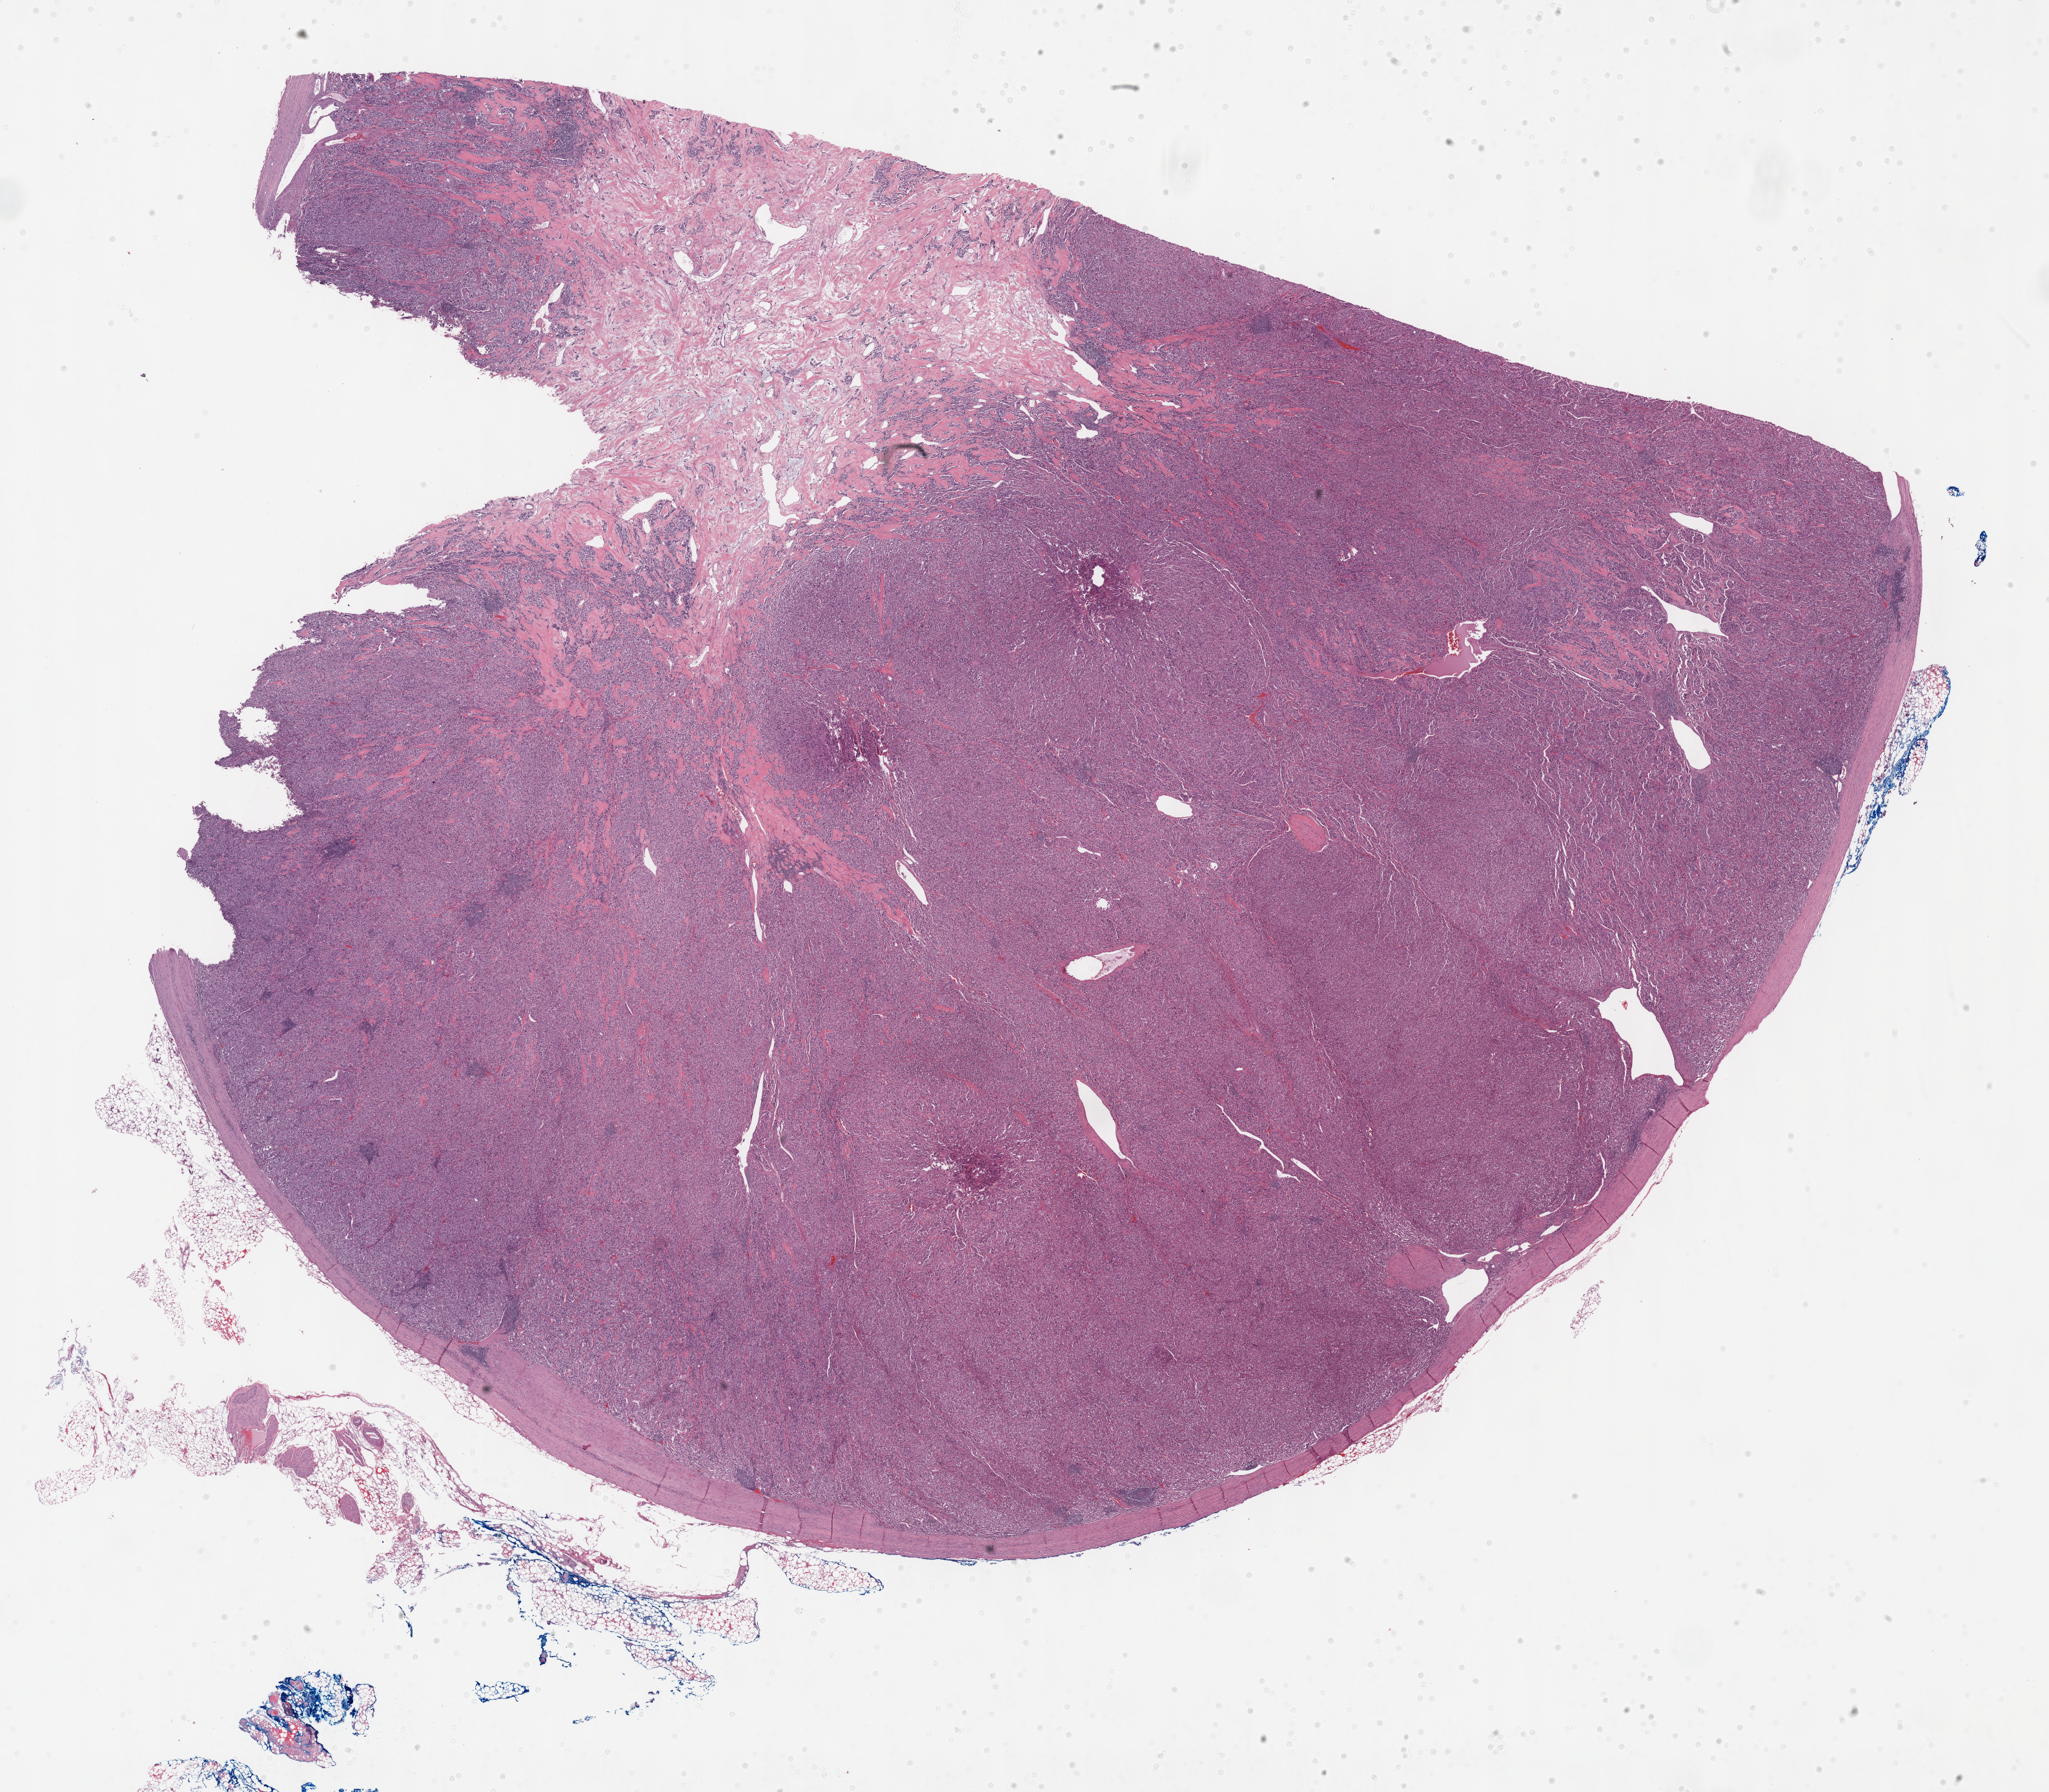
Digitized H&E-stained tissue section (whole slide), low-resolution overview of the scanned area, about 25.7 x 22.4 mm (from a 40x scan); formalin-fixed paraffin-embedded (FFPE) diagnostic section; adrenal gland, primary tumour sample. Female, age 51 years at initial diagnosis.
Diagnosis: Papillary adenocarcinoma, NOS (thyroid gland).